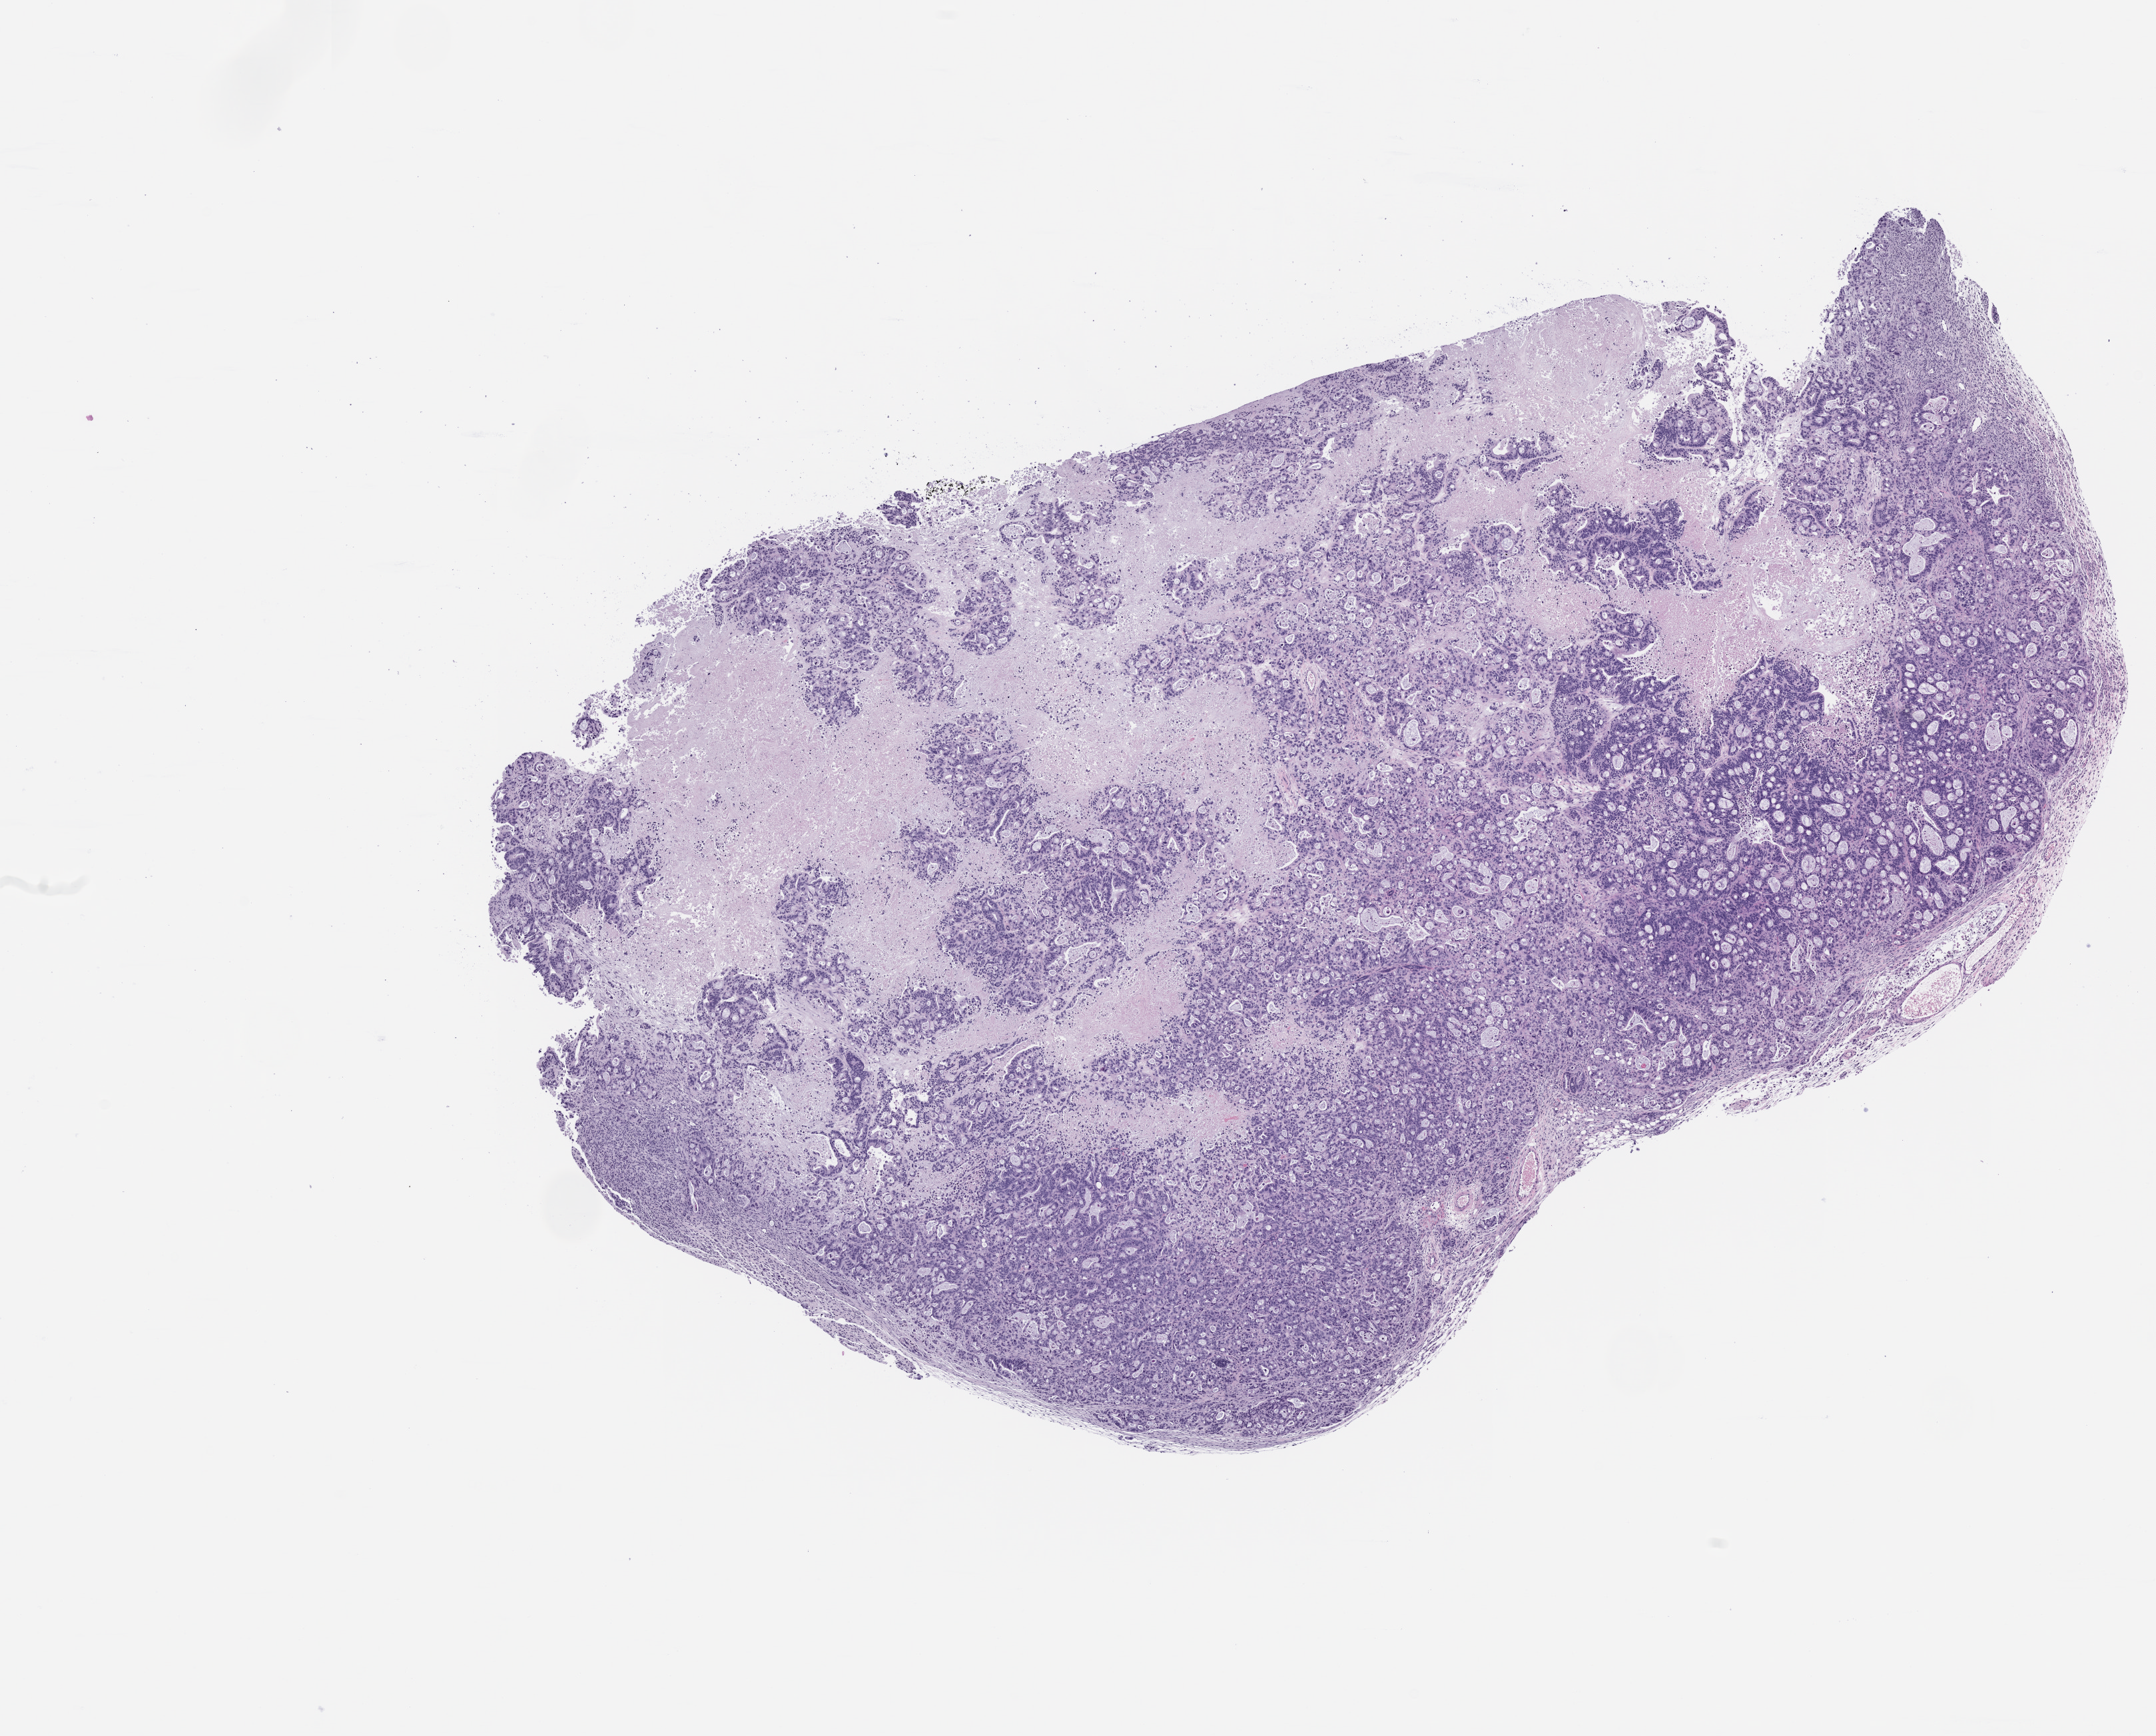
Whole-slide image, haematoxylin and eosin: patient-derived xenograft (human tumor grown in a mouse), passage 1, low-resolution overview of the scanned area, about 13.0 x 10.5 mm, formalin-fixed paraffin-embedded section, originating tumor site category: pancreas.
• originating patient diagnosis: Pancreatic Adenocarcinoma